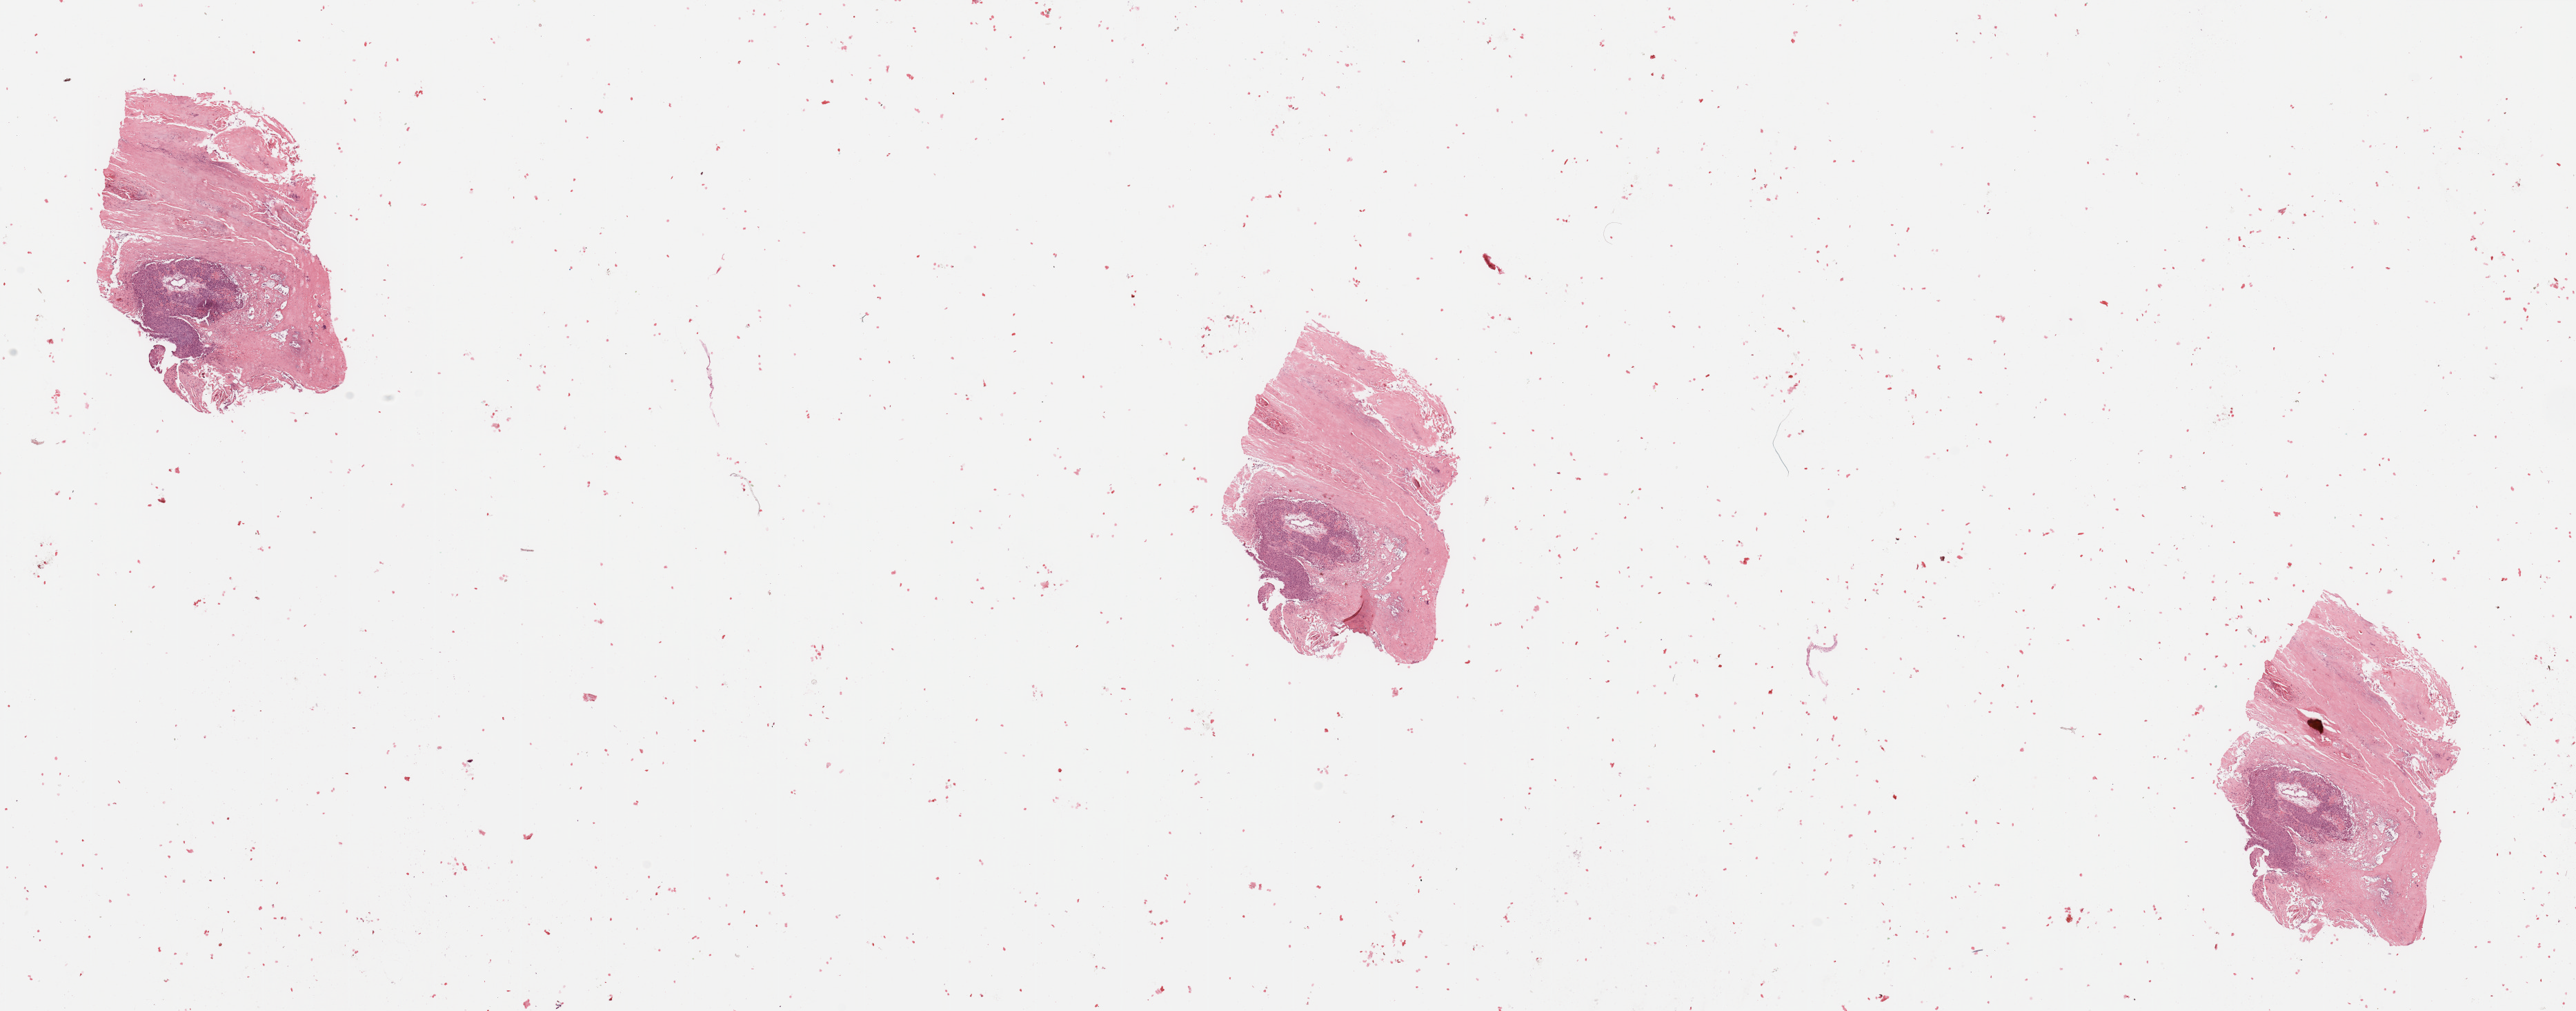
H&E-stained whole-slide image, a low-resolution overview of the entire scanned area, about 29.5 x 11.6 mm (slide scanned at 20x); head and neck, tissue type not recorded. Patient: male, age 56 years.
Patient diagnosis: Squamous cell carcinoma, NOS.